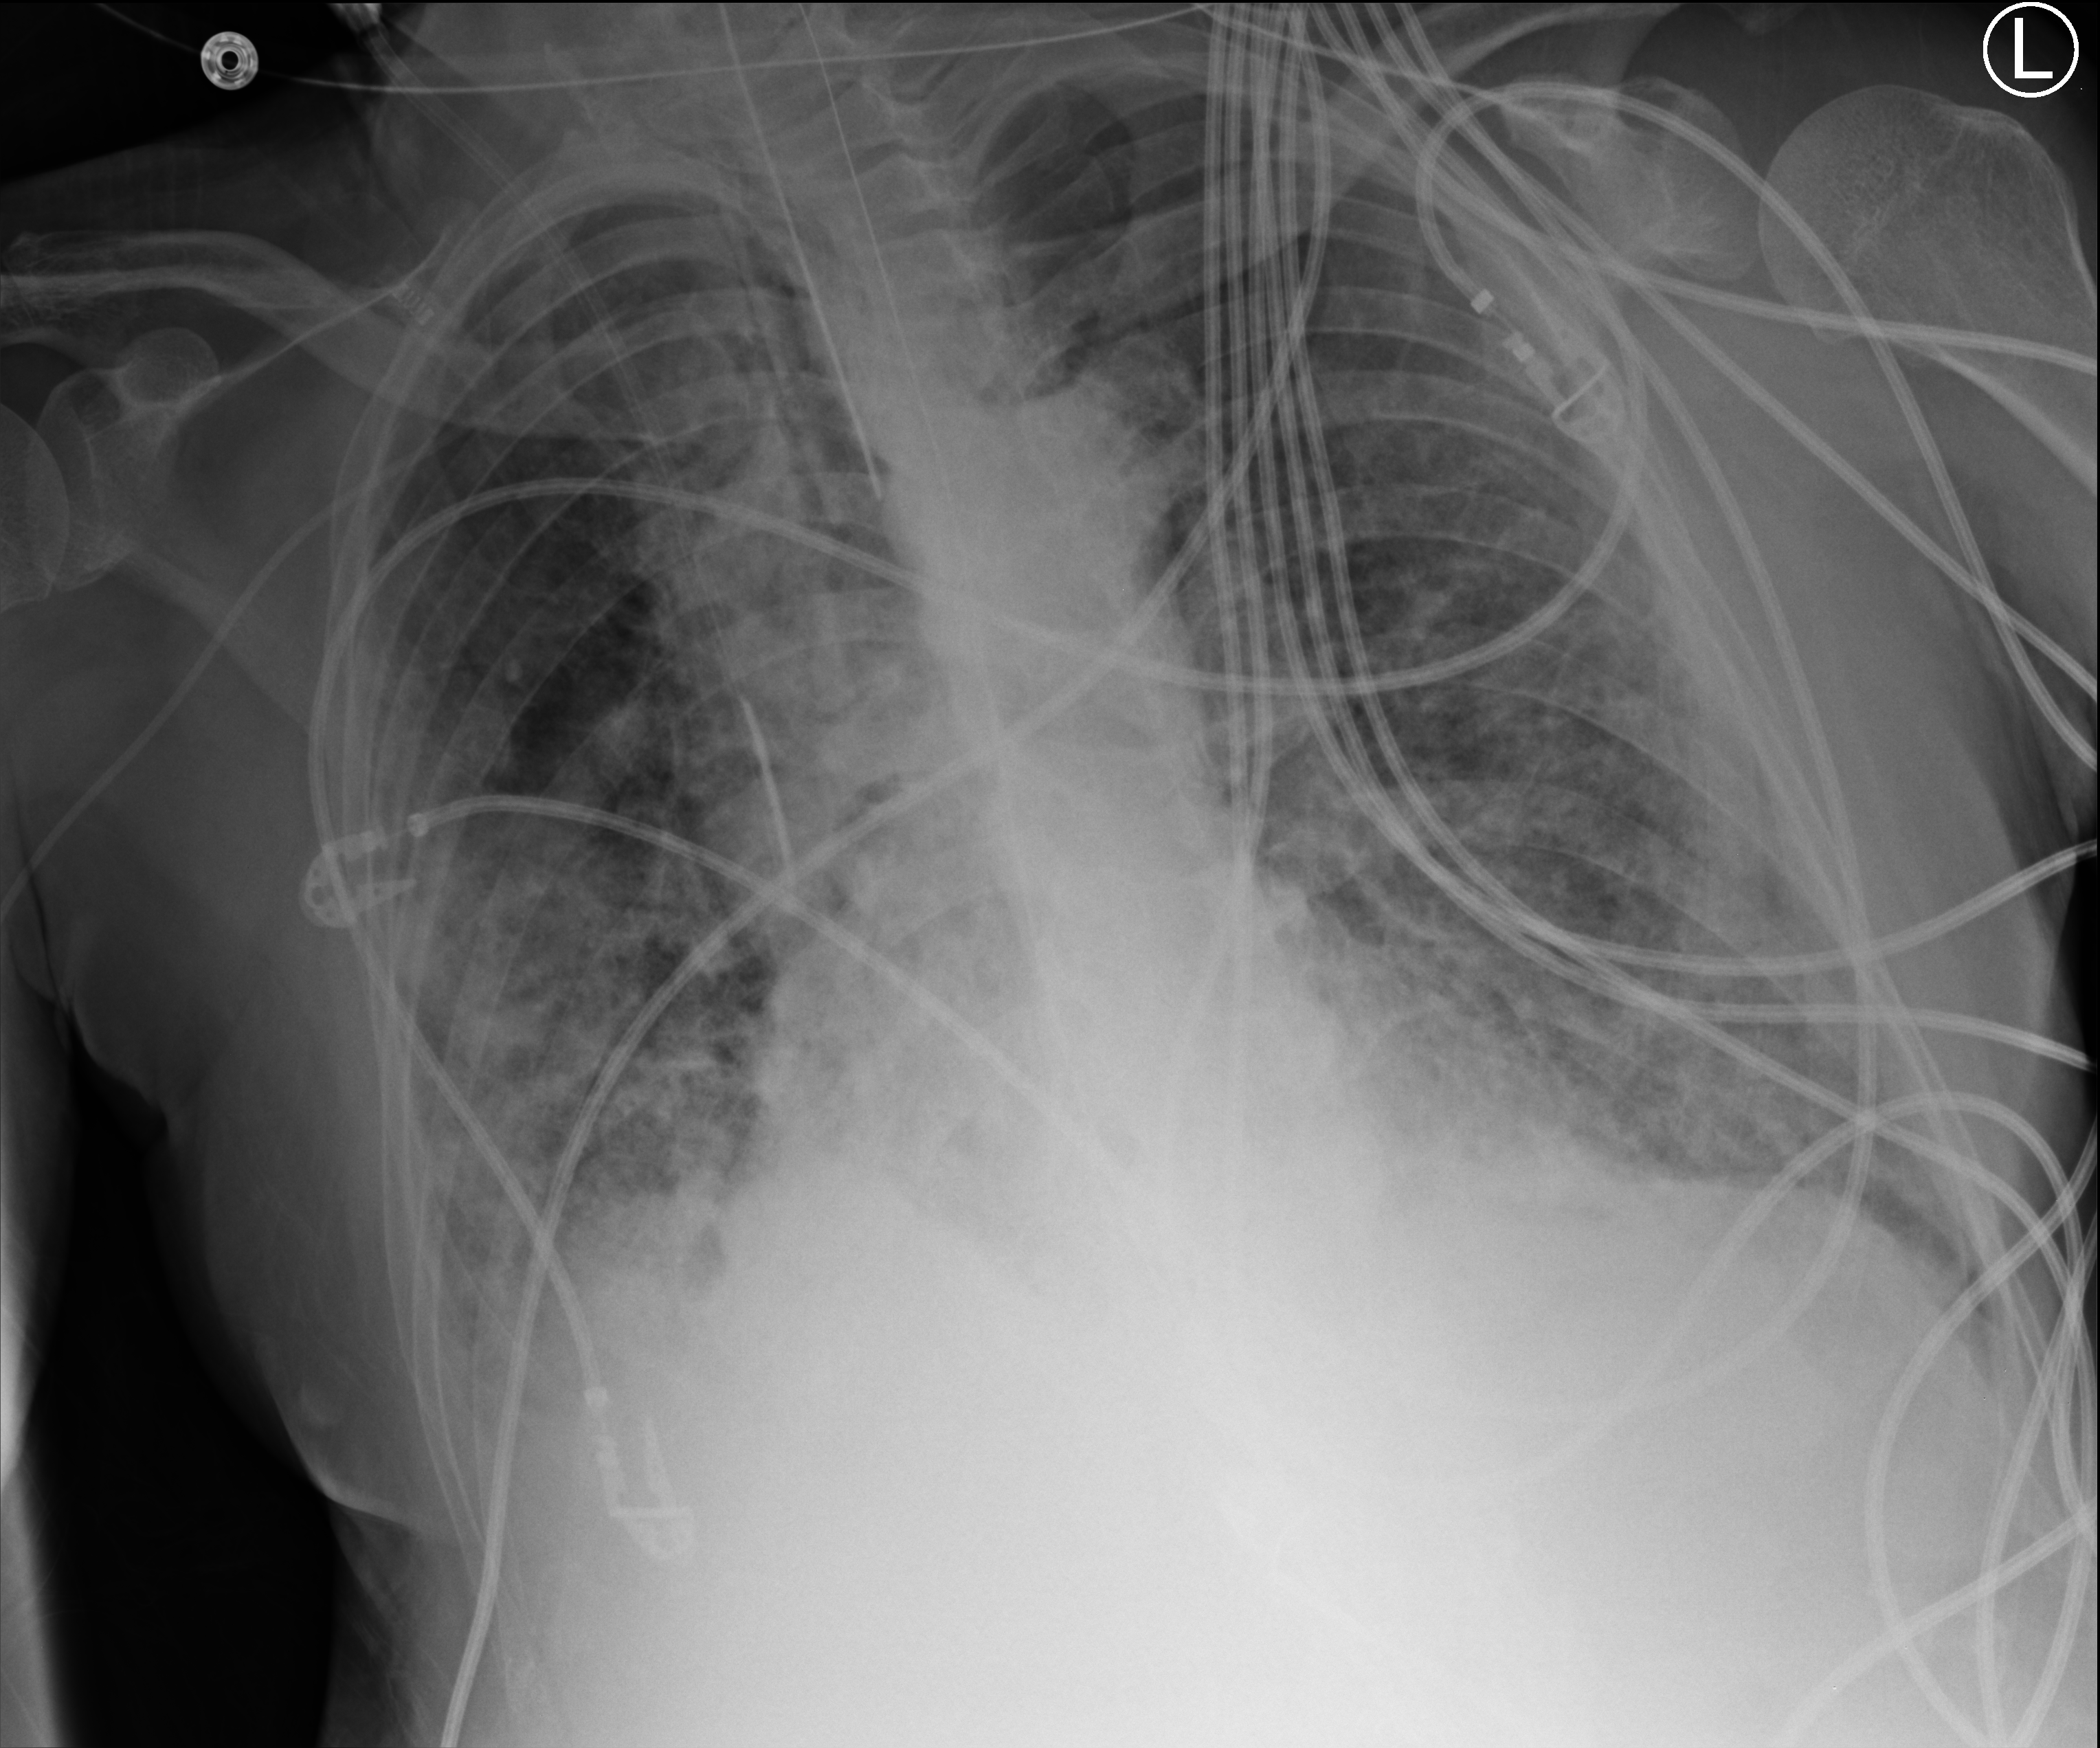
Chest X-ray (portable), anteroposterior (AP) projection. Patient hospitalised with COVID-19; male, aged 60–74 years.
Hospital-stay facts (about this admission, not read from this image; timing relative to this image not recorded):
- COPD (admission record): no